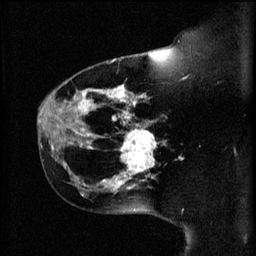
Breast MRI (dynamic contrast-enhanced), one sagittal slice. Position 43 of 60 along the scan axis. 3 images stored at this slice position (order not interpretable as contrast timing). 1.5 T. TE 4.2 ms, TR 11 ms. 2 mm slice thickness. 256 × 256 image matrix, field of view 180 × 180 mm. Patient: female, 44 years.
Structures marked on this image (semi-automatically segmented with operator editing):
- analysis volume of interest (the breast-tissue region the enhancement analysis was run in; not a lesion): bounding box <114,124,165,179> (left, top, right, bottom; pixels)
- tumour enhancement mask (voxels above the 70 % enhancement threshold inside the analysis volume of interest): <116,130,157,179>